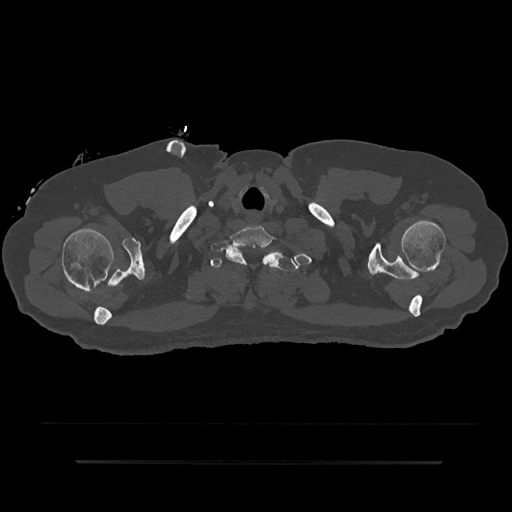
CT including the spine, one axial slice. Slice 758 of 797 in the series (ordered by position). Reconstruction kernel Br40s/3. Bone window (W 1800 / L 400 HU). 0.5 mm slice thickness. 512 × 512 image matrix, field of view 464 × 464 mm. Male patient, age 59 years. Case-level facts recorded for this patient, not image findings: primary cancer: bile ducts.
Structures marked on this image (semi-automatic segmentation, software-assisted and operator-edited):
- T1 vertebra: bounding box [x1, y1, x2, y2] px = [210, 252, 300, 271]